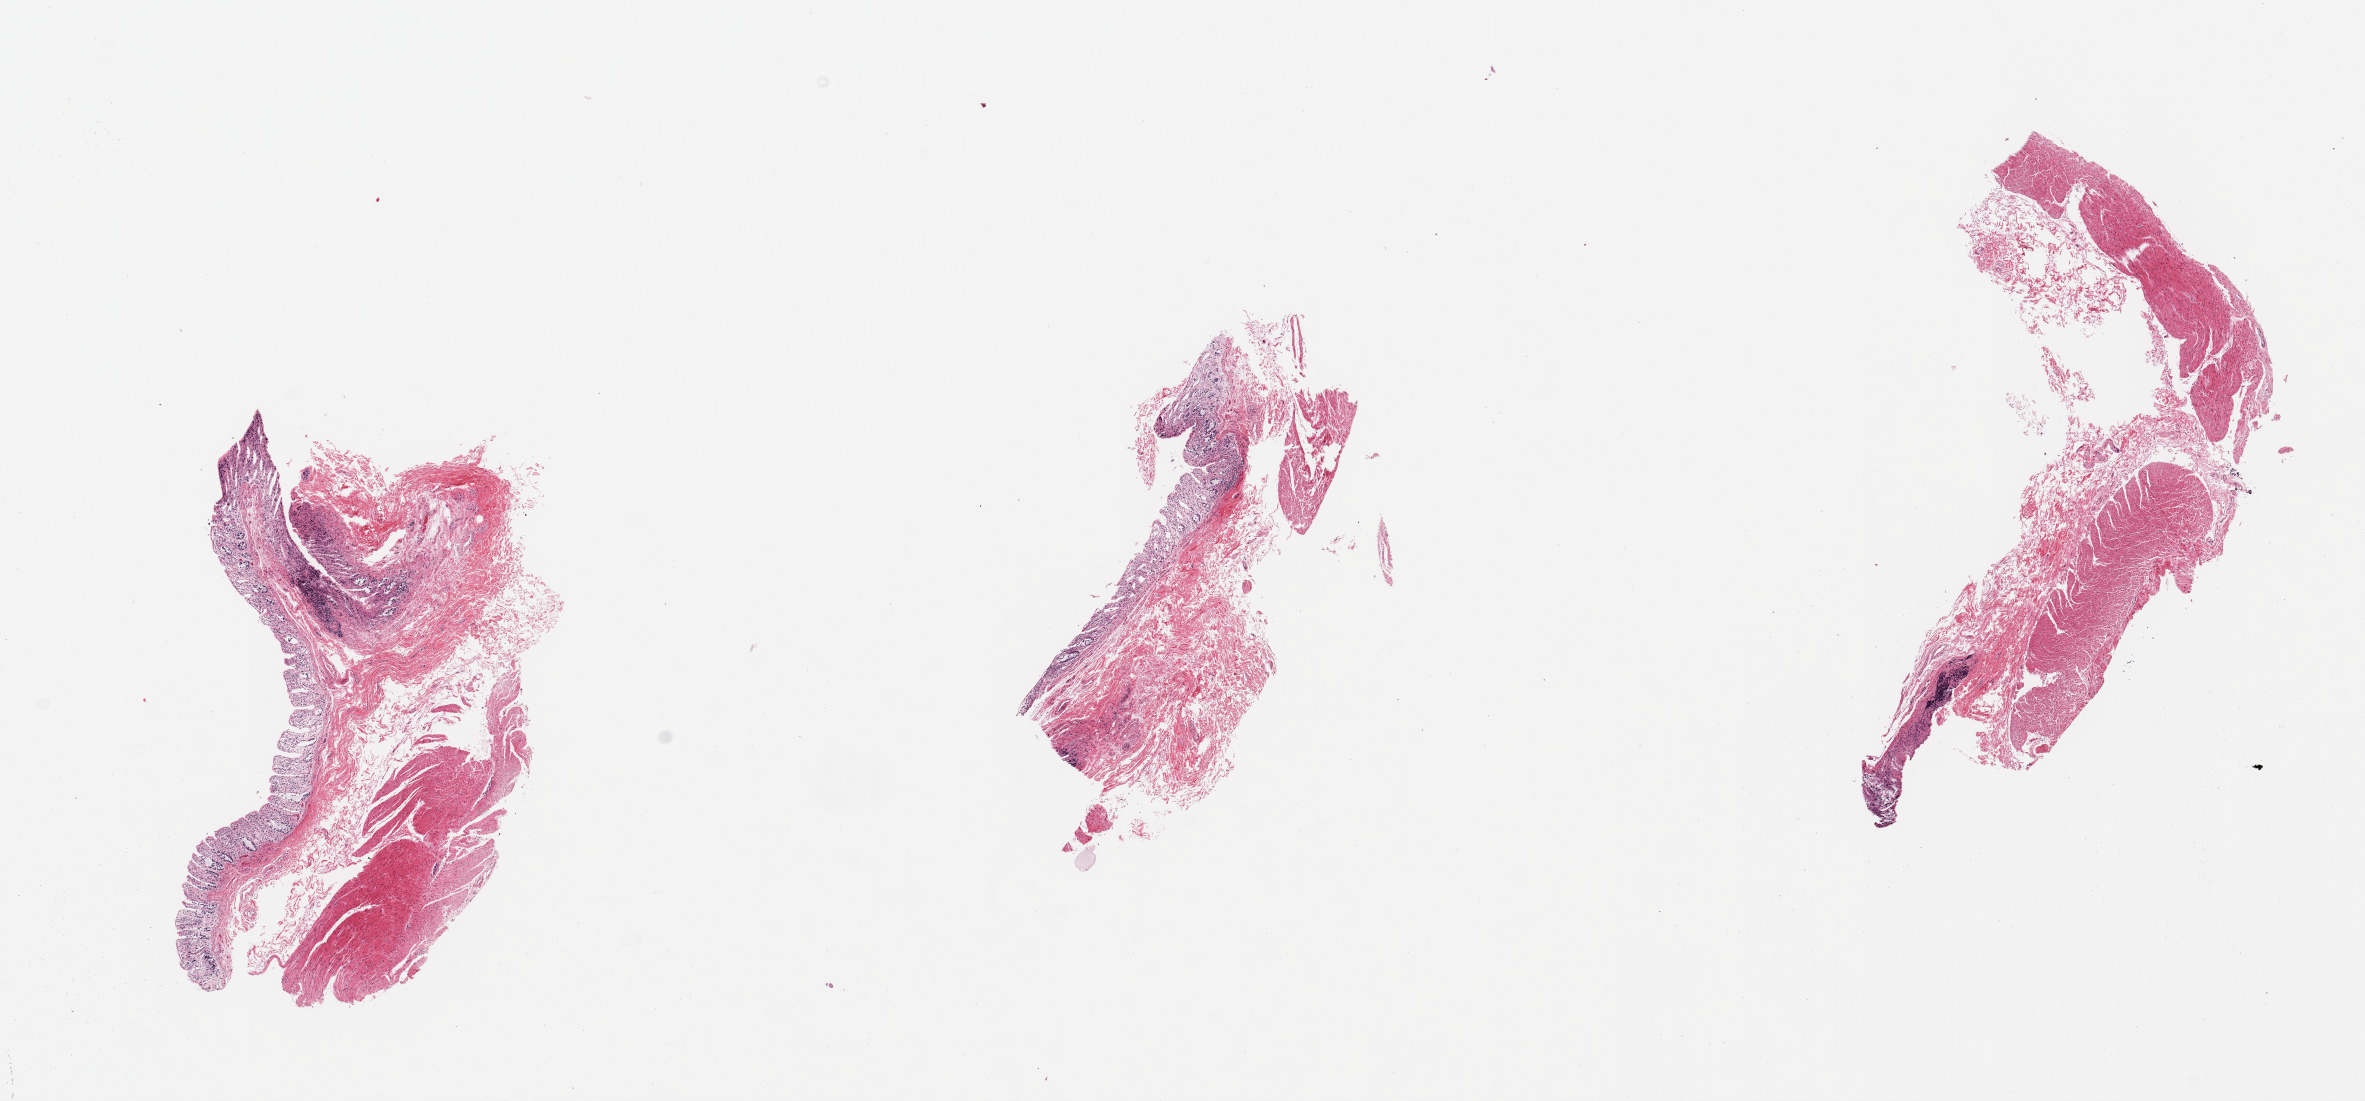
Whole-slide image, hematoxylin and eosin (H&E) stain — low-resolution overview of the scanned area, about 18.7 x 8.7 mm (acquisition: 20x scan). PAXgene-fixed paraffin-embedded (PFPE) section. Section of sigmoid colon (target tissue). Tissue donor sample.
Reviewer comment on this tissue sample: 3 pieces ~10% 'contaminant'.